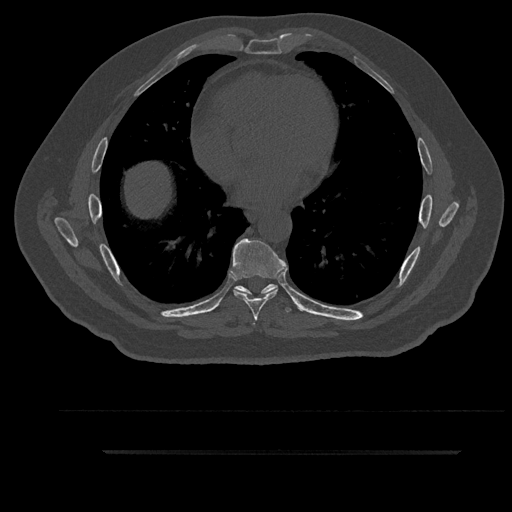
CT including the spine, one axial slice; position 510 of 797 along the scan axis; reconstruction kernel Br40s/3; bone window (W 1800 / L 400 HU); 0.5 mm slice thickness; 512 × 512 image matrix, field of view 432 × 432 mm. Patient: male, 63 years. From the clinical record (not read from this slice): primary cancer: renal.
Annotated regions visible in this slice (semi-automatic segmentation, software-assisted and operator-edited):
- T6 vertebra: bounding box <234,288,270,325> (left, top, right, bottom; pixels)
- T7 vertebra: <231,238,288,321>
- T8 vertebra: <235,284,291,312>